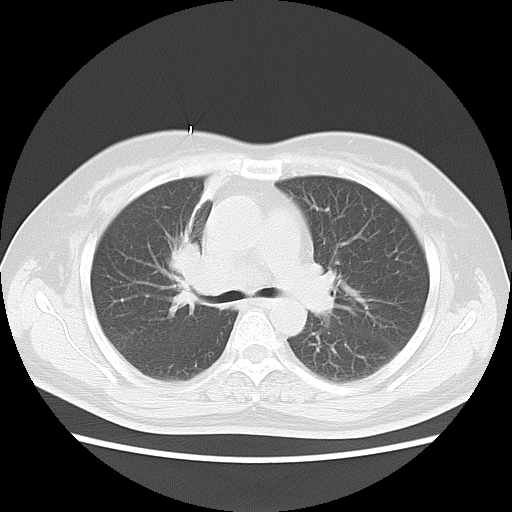
Chest CT, one axial slice; slice 6 of 18 in the series (ordered by position); 120 kVp; lung window (W 1500 / L -600 HU); 512 × 512 image matrix, field of view 350 × 350 mm. Patient: female, 54 years. From the clinical record (not read from this slice): clinical TNM (as recorded): T2 N3 M0; histopathological grade: G3.
Structures marked on this image (rectangle marked by the reading radiologist):
- lung tumour (recorded histology: small cell carcinoma): bounding box [x1, y1, x2, y2] px = [156, 233, 207, 327]